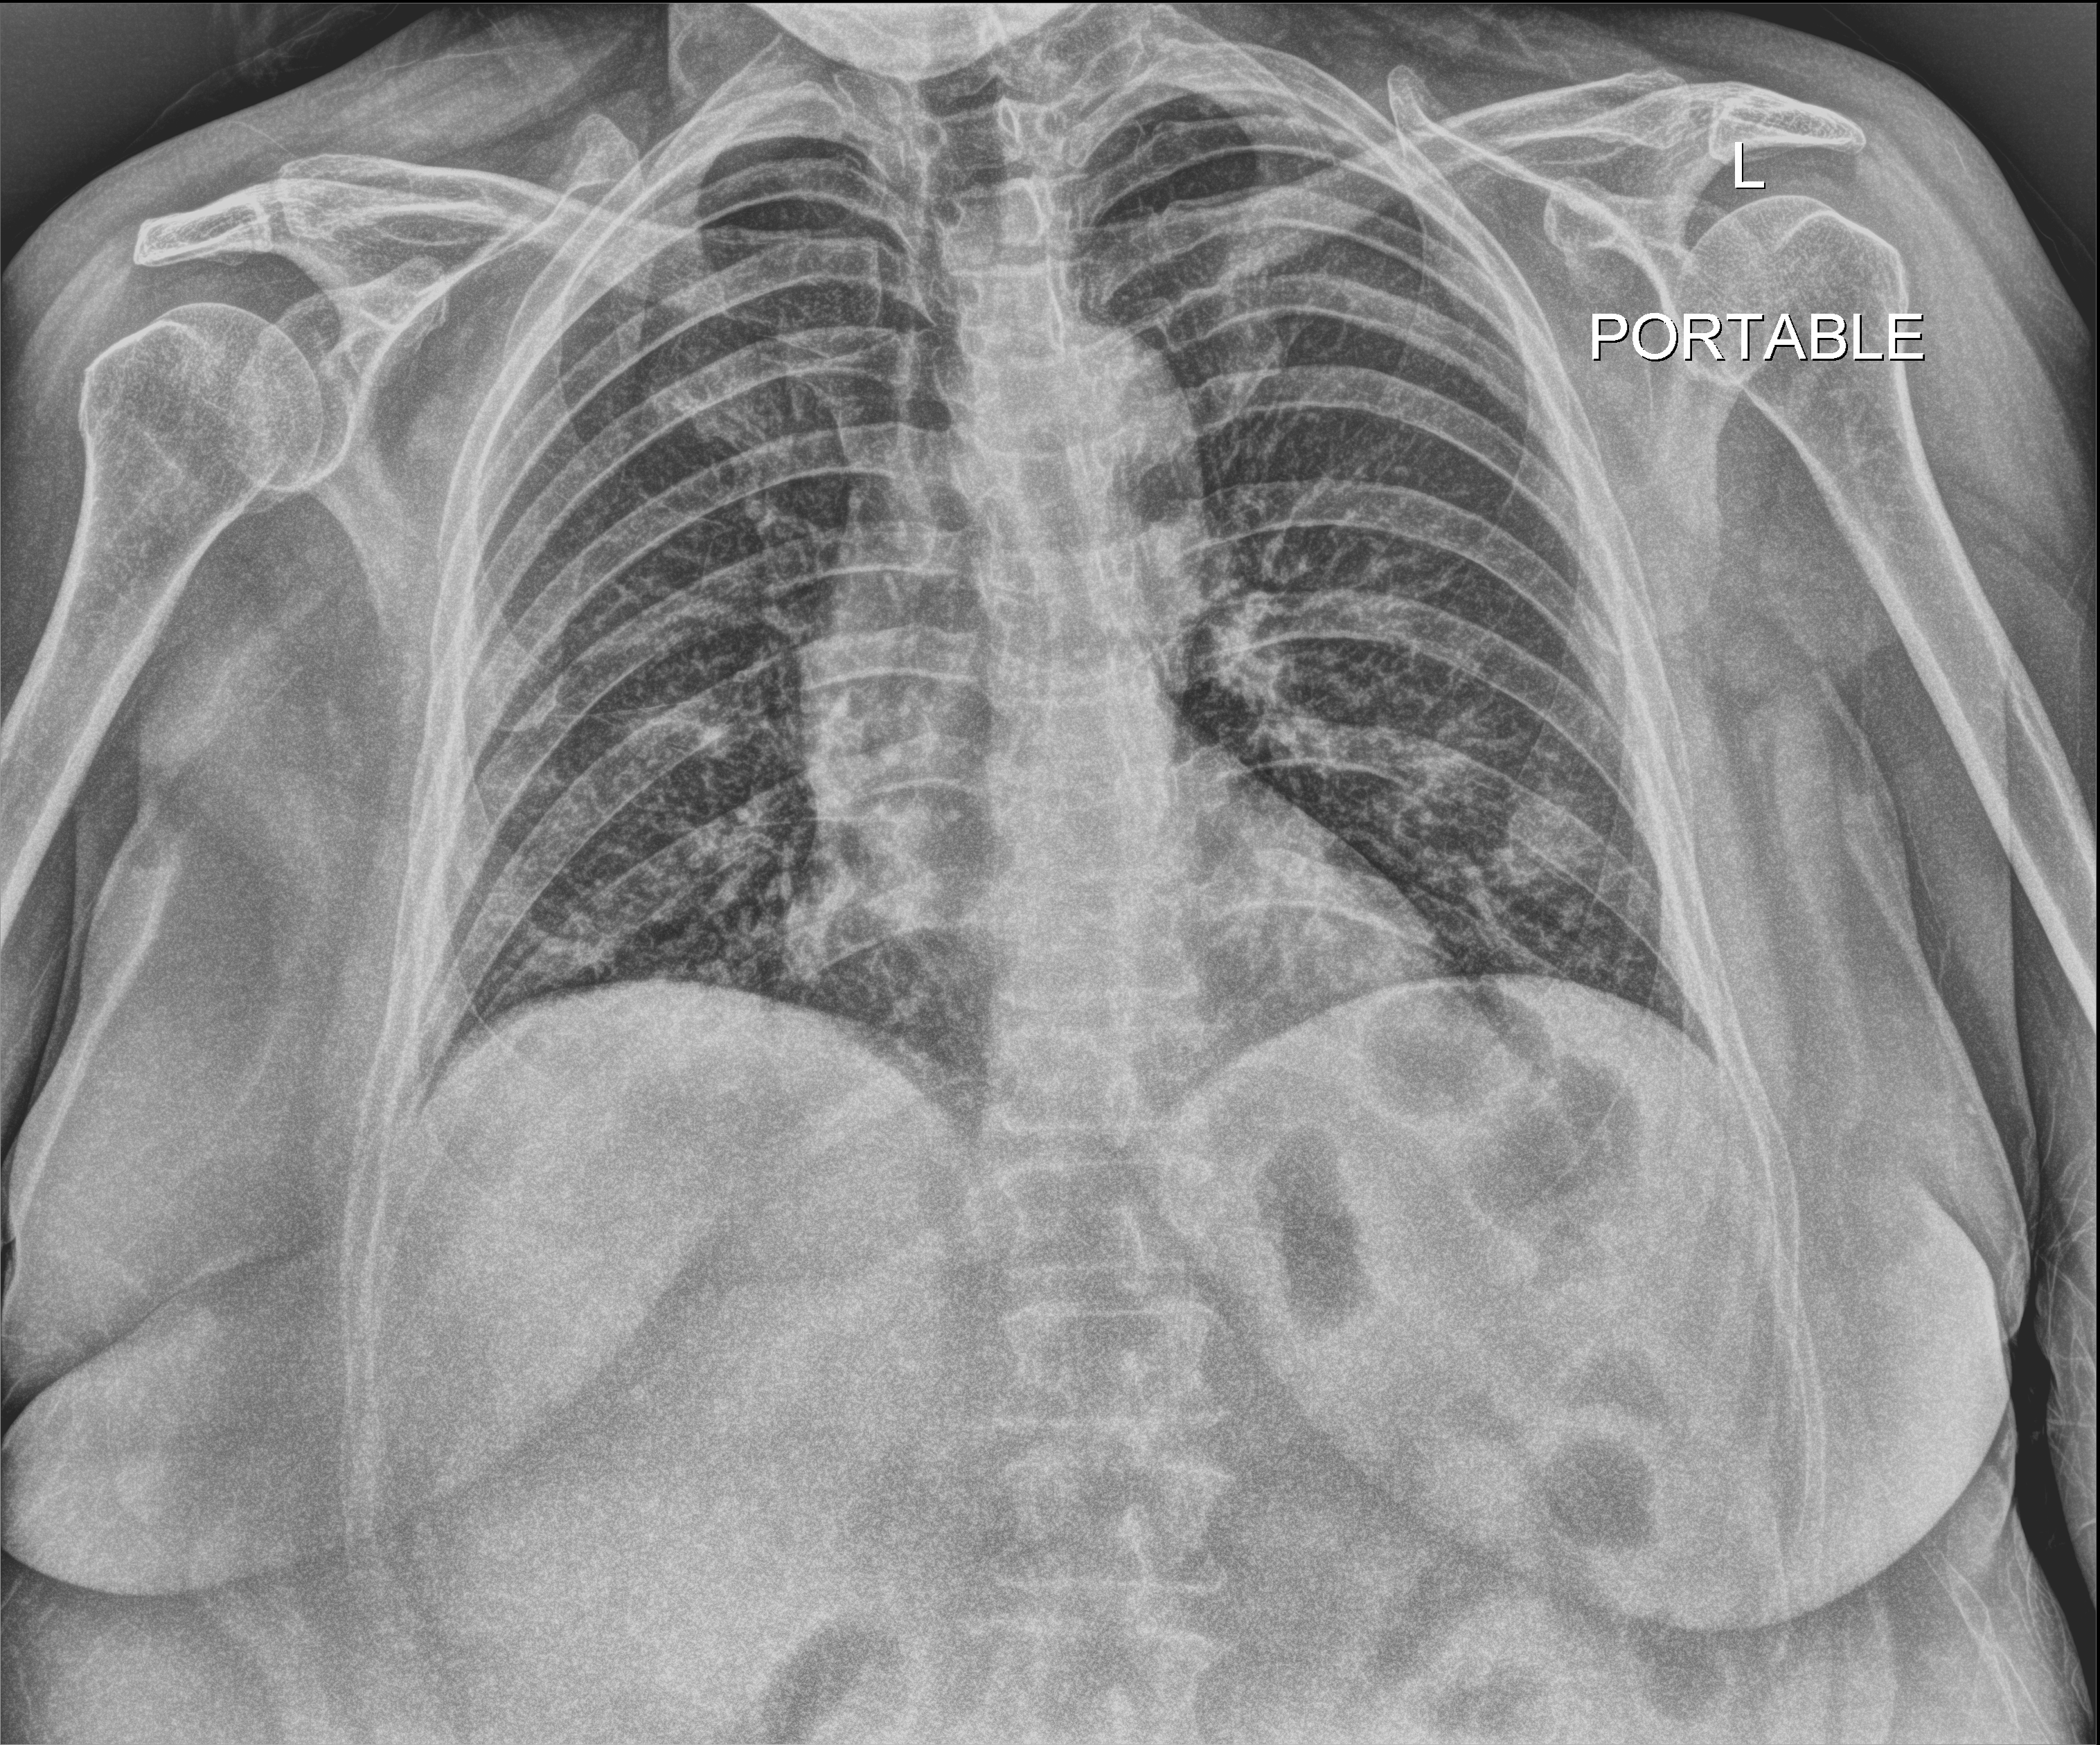
Chest X-ray; anteroposterior (AP) projection. Patient hospitalised with COVID-19; female, aged 60–74 years.
From the hospital-stay record, not from the radiograph (when in the stay this image was taken is not recorded): admitted to intensive care during this hospital stay: no.